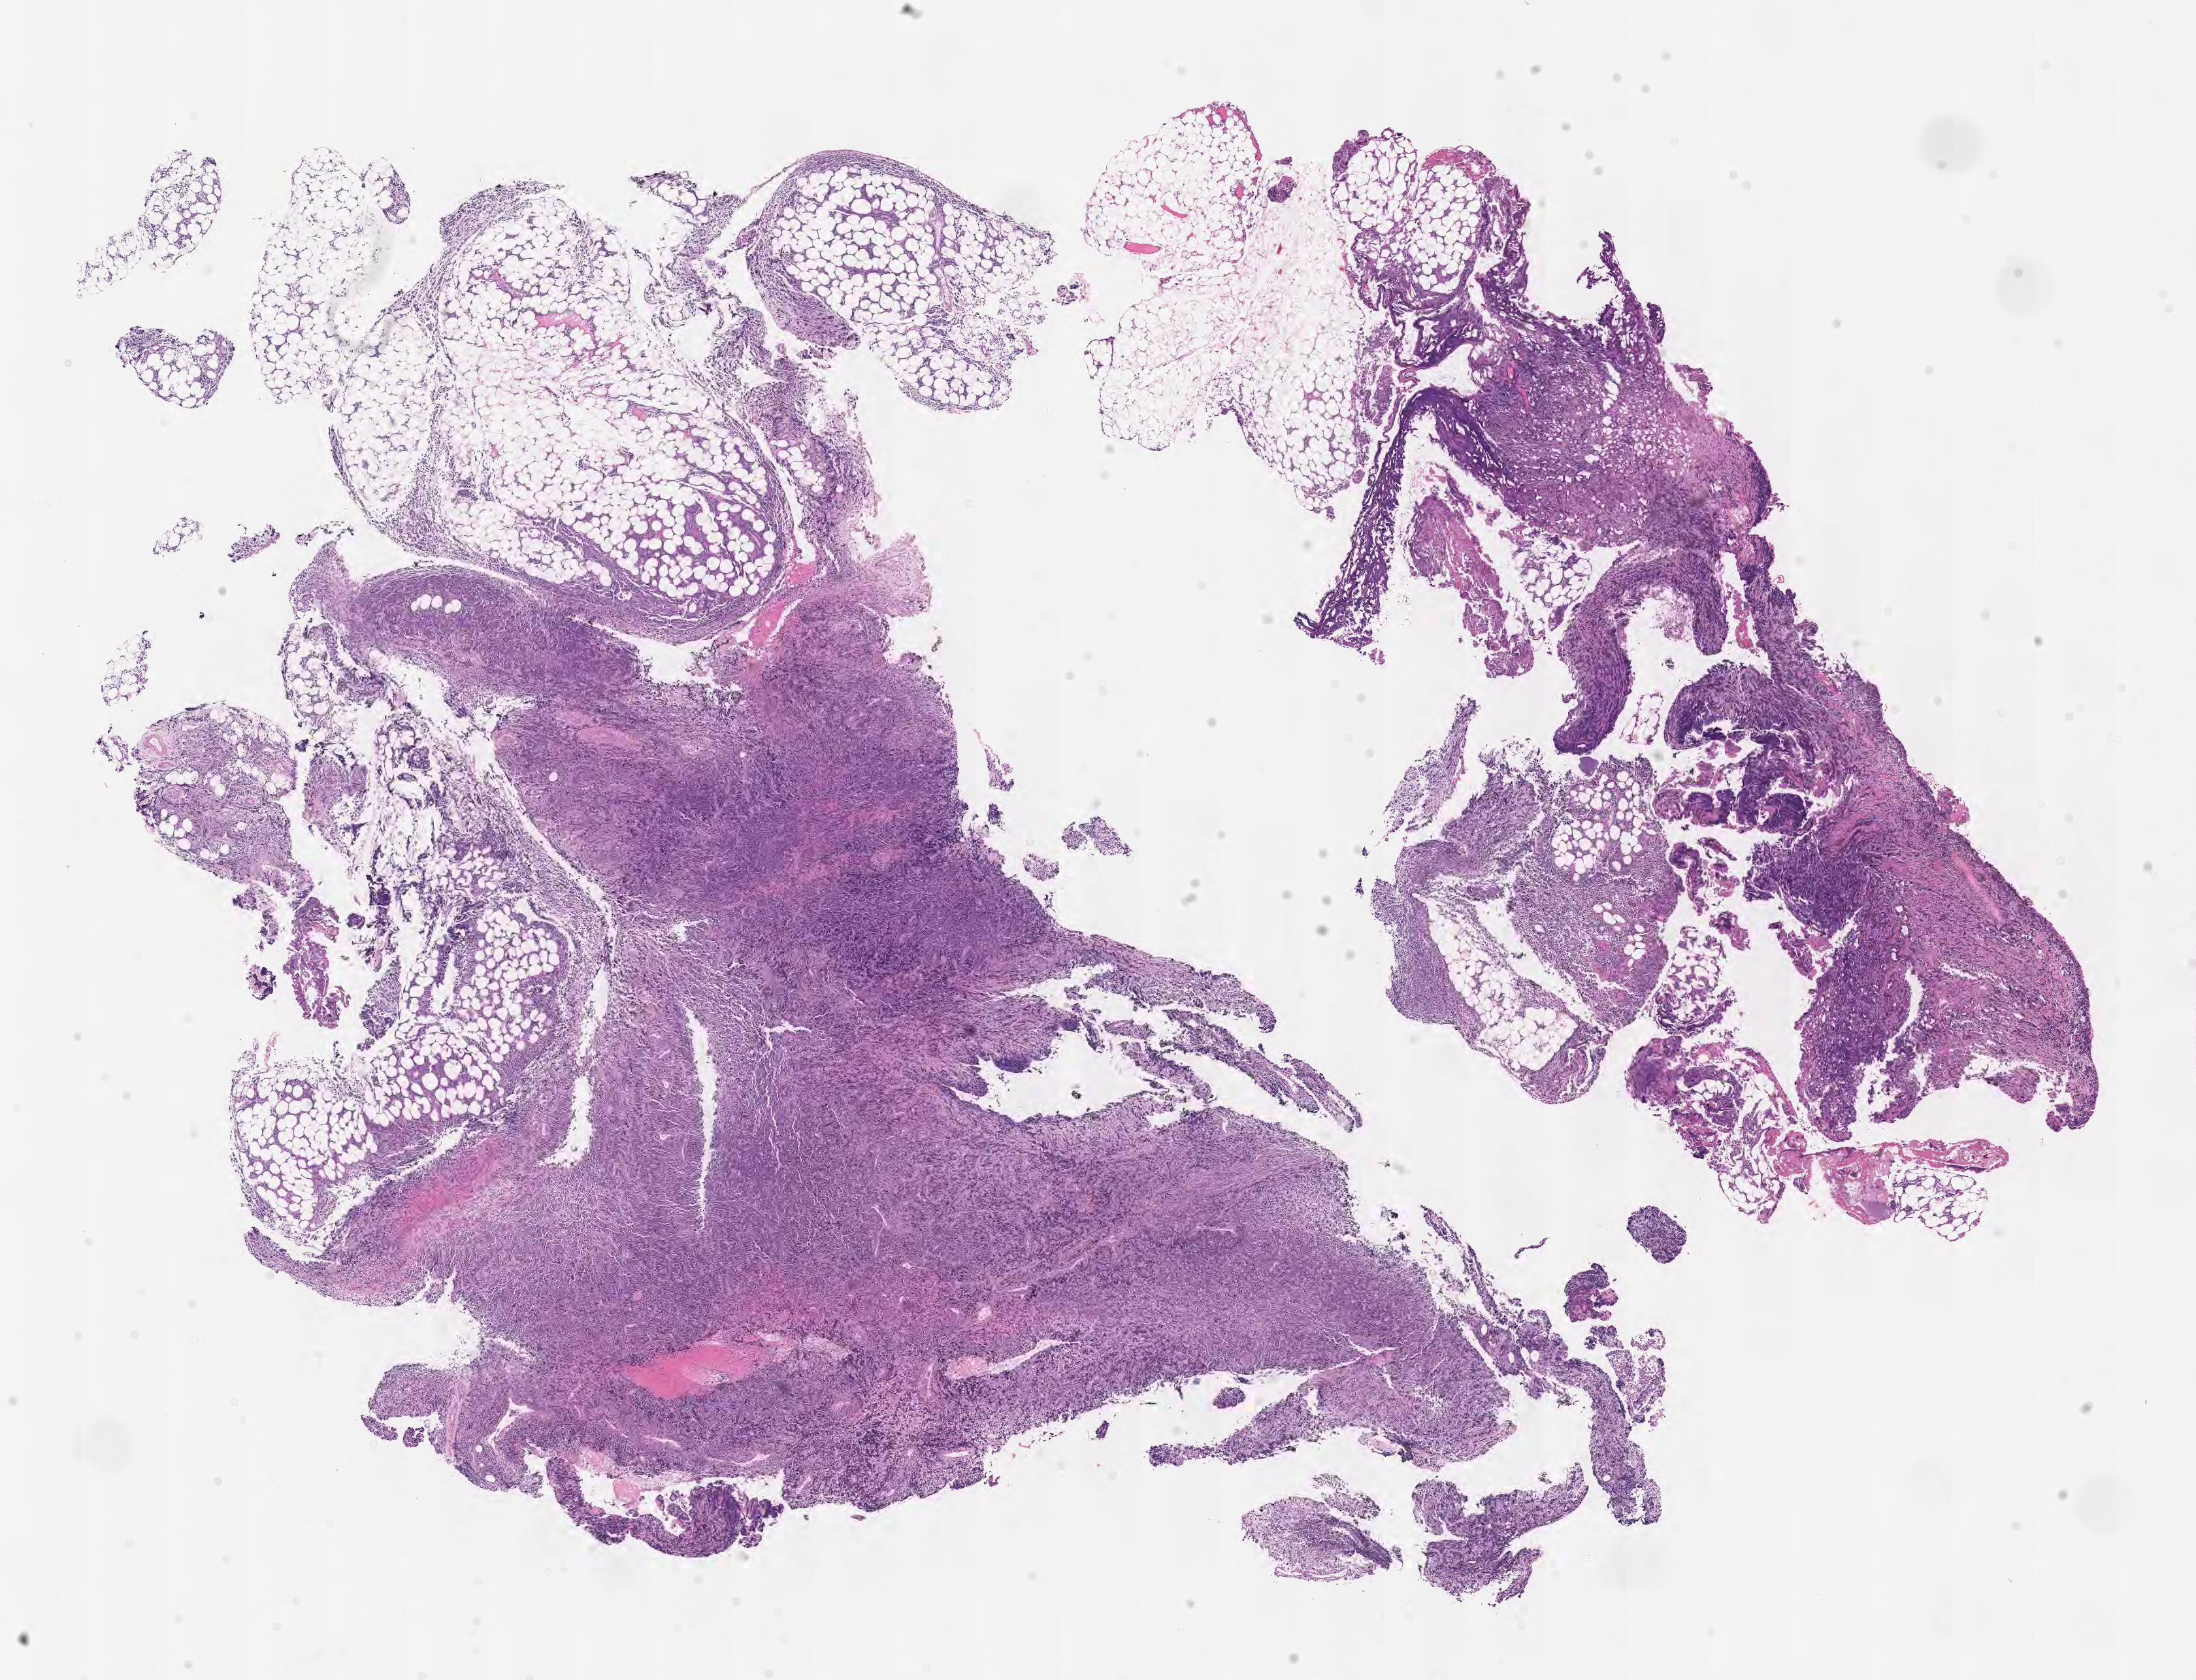
Whole-slide image, hematoxylin and eosin (H&E) stain — low-resolution overview of the scanned area, about 13.6 x 10.4 mm; specimen: tumor tissue; site: abdominal lymph node. Male patient; age at initial diagnosis 9 years.
Diagnosis: Burkitt lymphoma, NOS.